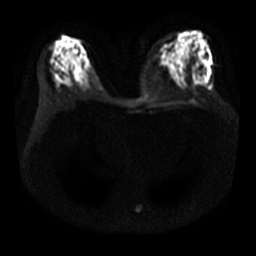
Breast MRI, one axial slice; position 13 of 29 along the scan axis; diffusion-weighted series; image 2 of 4 stored at this slice position (different b-values; order by instance number); 3 T; 5 mm slice thickness; 256 × 256 image matrix. Female patient.
Structures marked on this image (manually delineated by an expert):
- tumour on diffusion-weighted imaging: bounding box (x1, y1, x2, y2) in pixels: (202, 75, 205, 78)